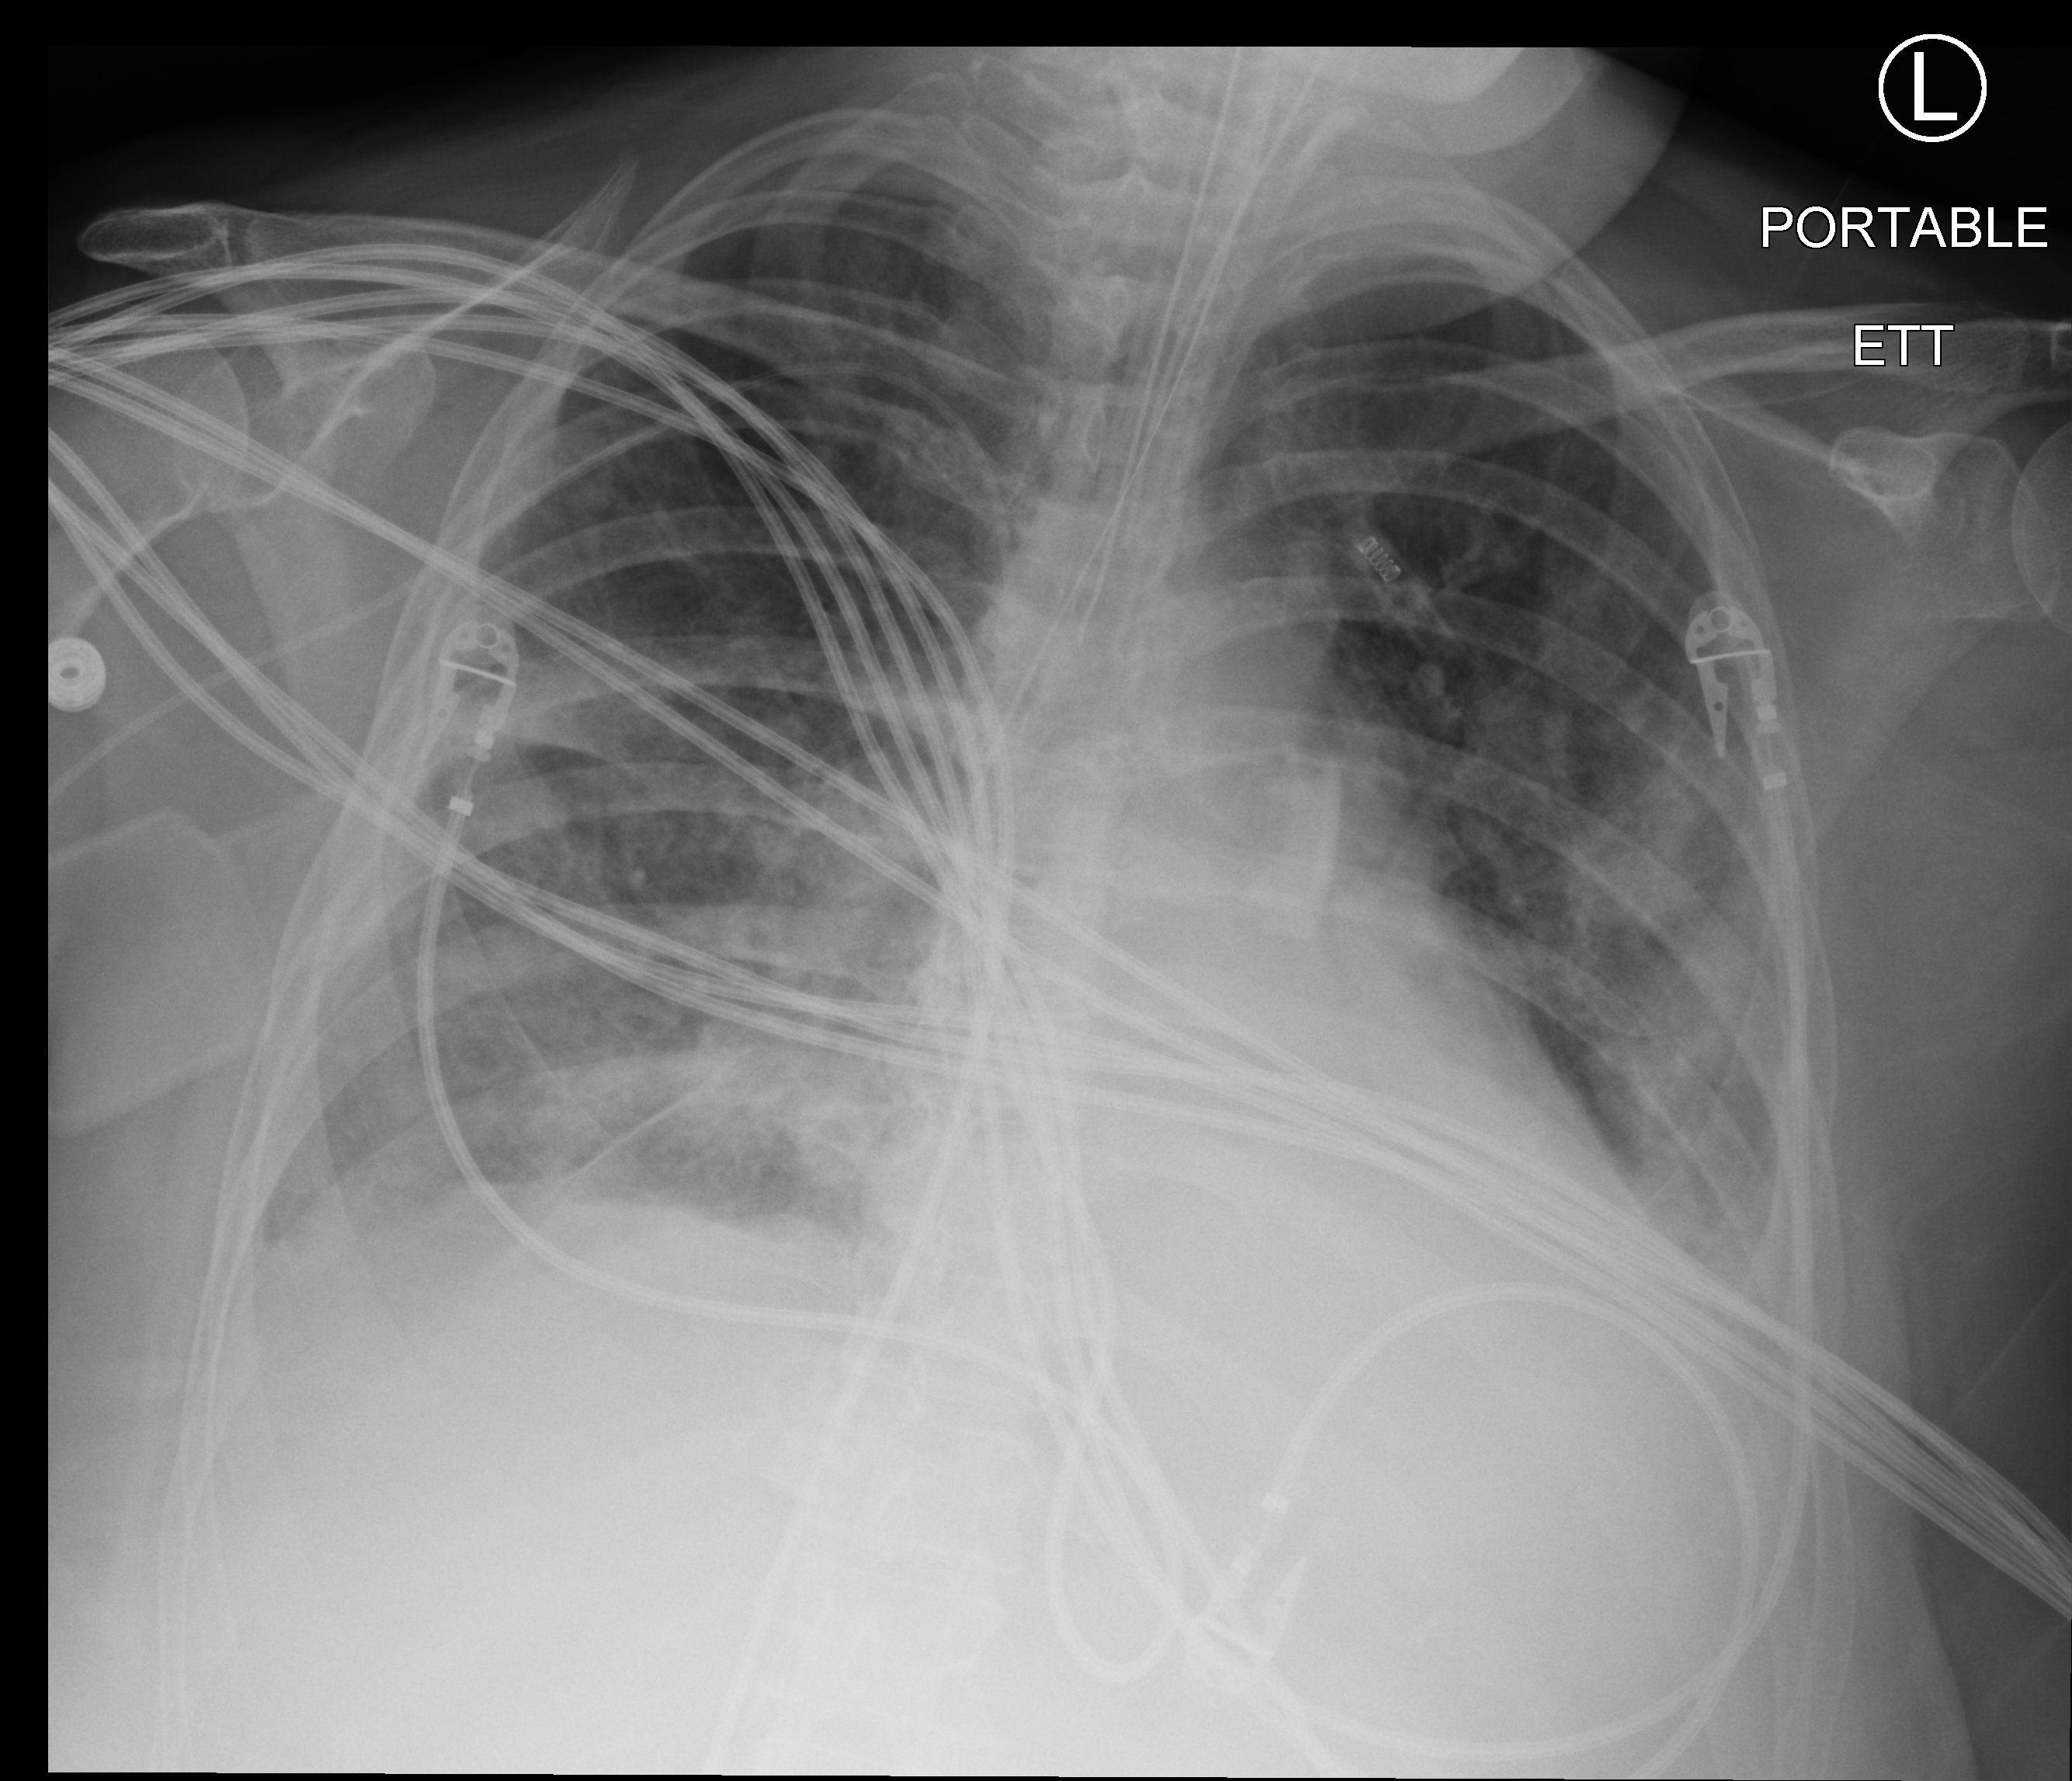
Chest X-ray (portable). Female patient hospitalised with COVID-19, age 60–74 years.
Hospital-stay facts (about this admission, not read from this image; timing relative to this image not recorded):
- admitted to intensive care during this hospital stay: yes